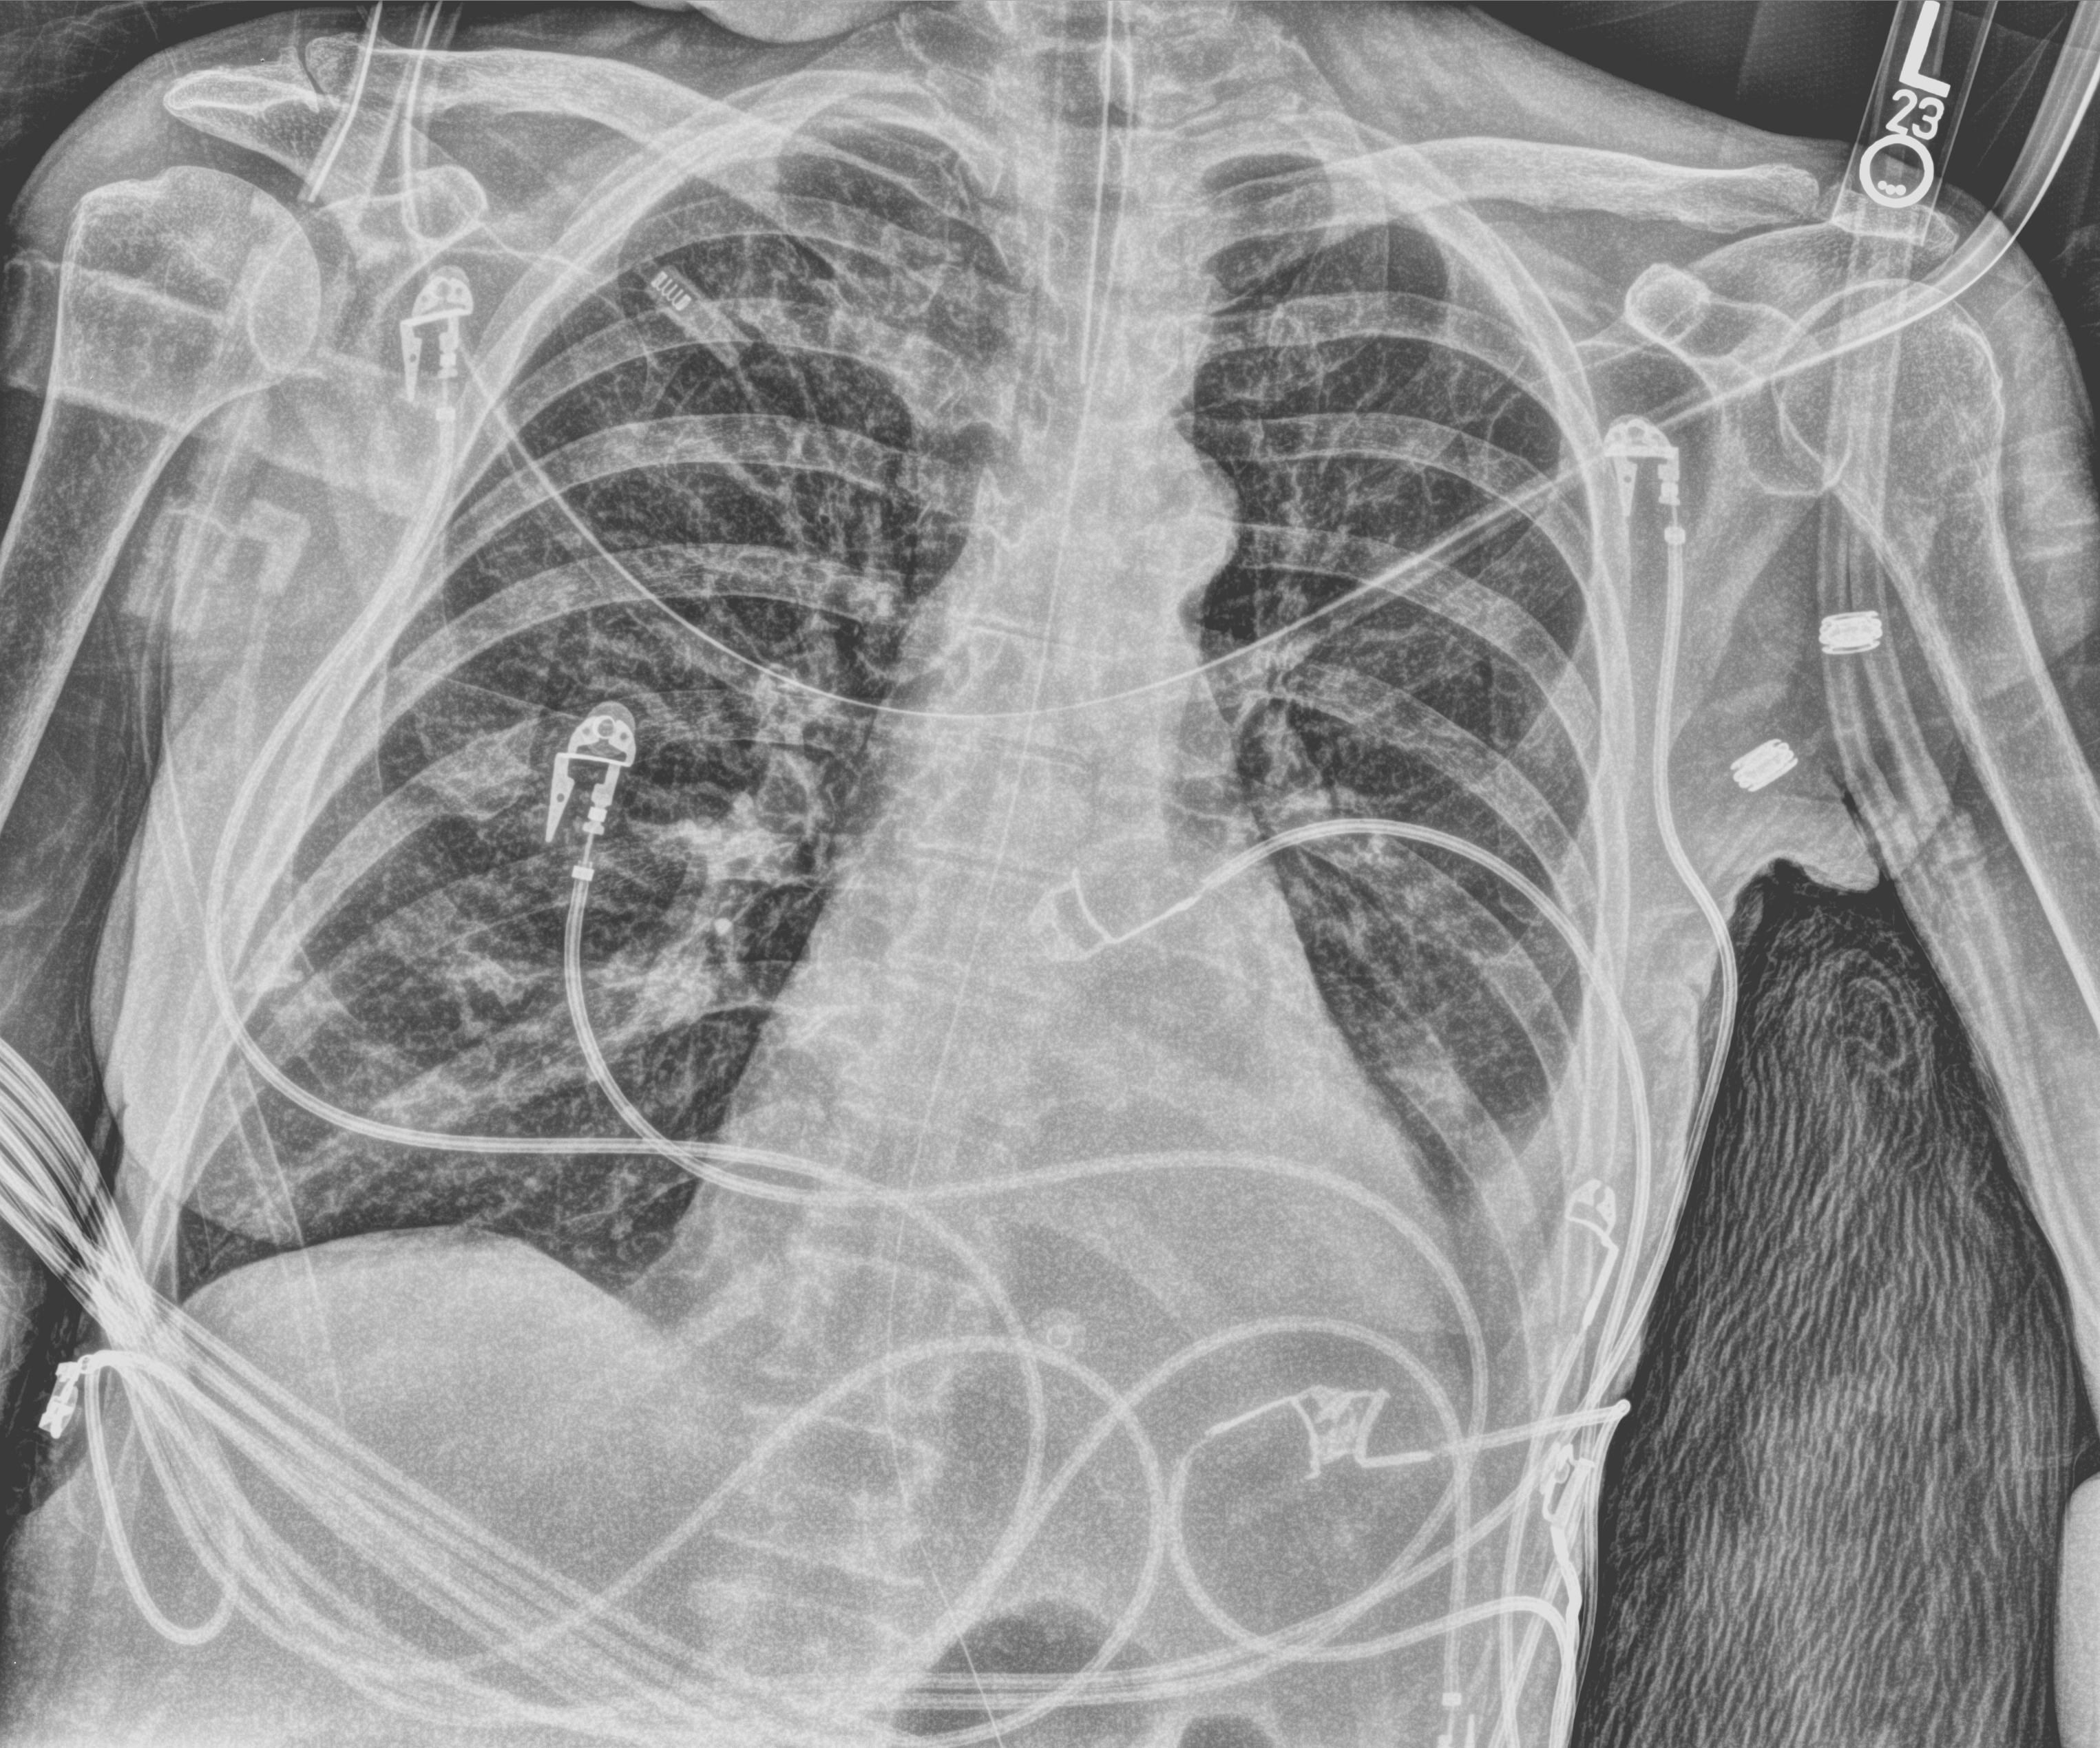
Chest X-ray (portable), anteroposterior (AP) projection. Female patient hospitalised with COVID-19, age 60–74 years.
Admission-level facts for this patient (not findings on this image; timing relative to this image not recorded):
- admitted to intensive care during this hospital stay: yes